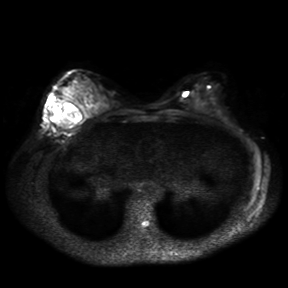
Breast MRI, one axial slice; position 17 of 30 along the scan axis; diffusion-weighted series; image 2 of 4 stored at this slice position (different b-values; order by instance number); 3 T; 4 mm slice thickness; 288 × 288 image matrix, field of view 360 × 360 mm. Female patient.
Structures marked on this image (expert manual segmentation):
- tumour on diffusion-weighted imaging: bounding box [x1, y1, x2, y2] px = [48, 101, 69, 129]